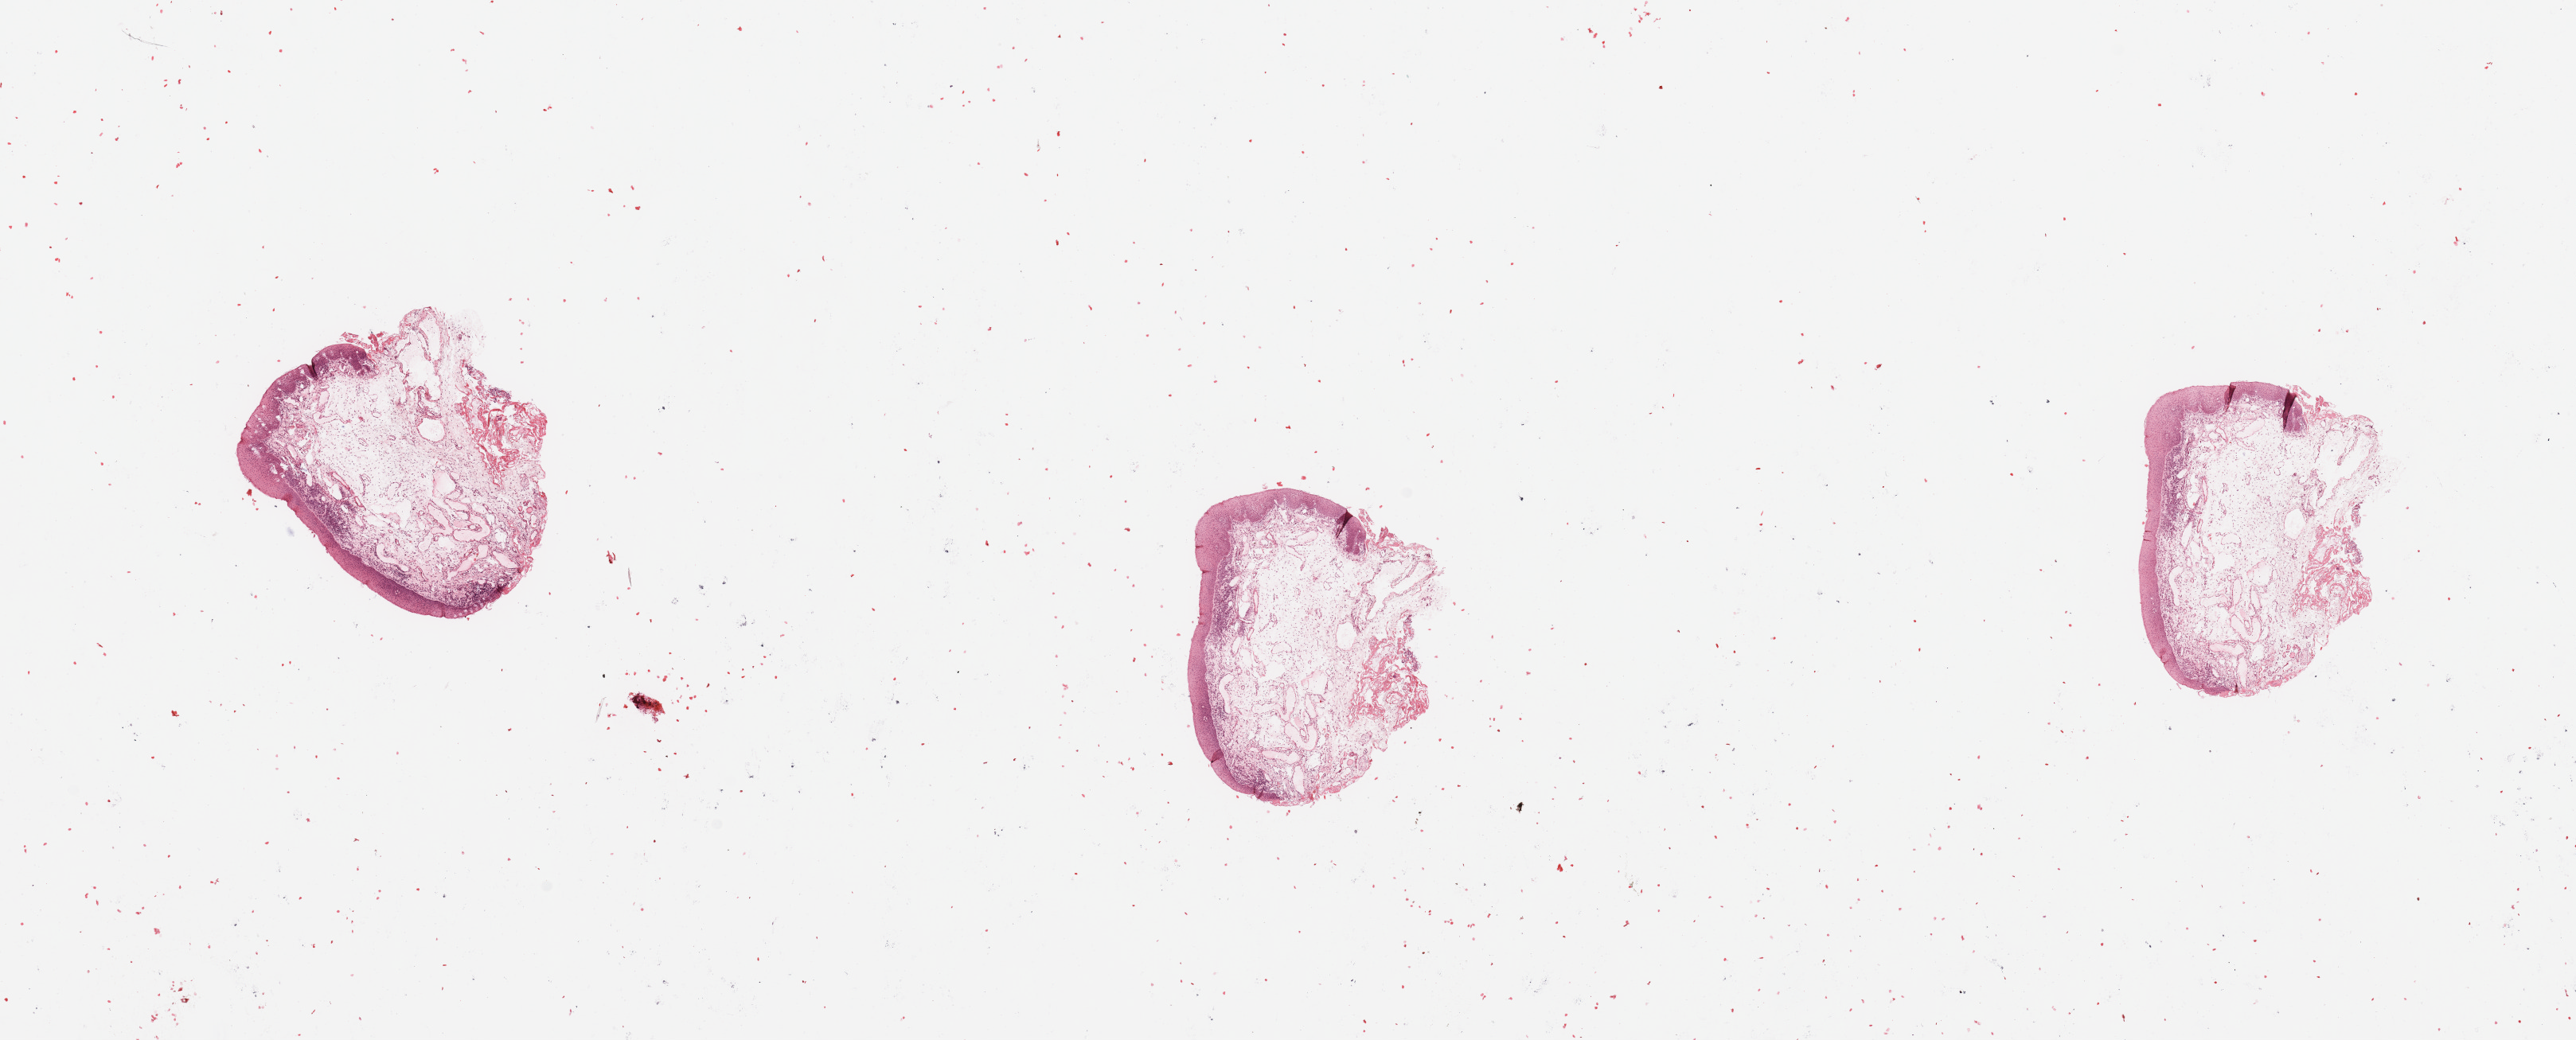
Digitized H&E tissue section (whole slide), a low-resolution overview of the entire scanned area, about 25.6 x 10.3 mm (acquisition: 20x scan), normal (non-tumour) tissue sample, sampled site: larynx. 59-year-old male patient.
This section: normal (non-tumour) tissue from the same patient. Patient diagnosis: Squamous cell carcinoma, NOS.